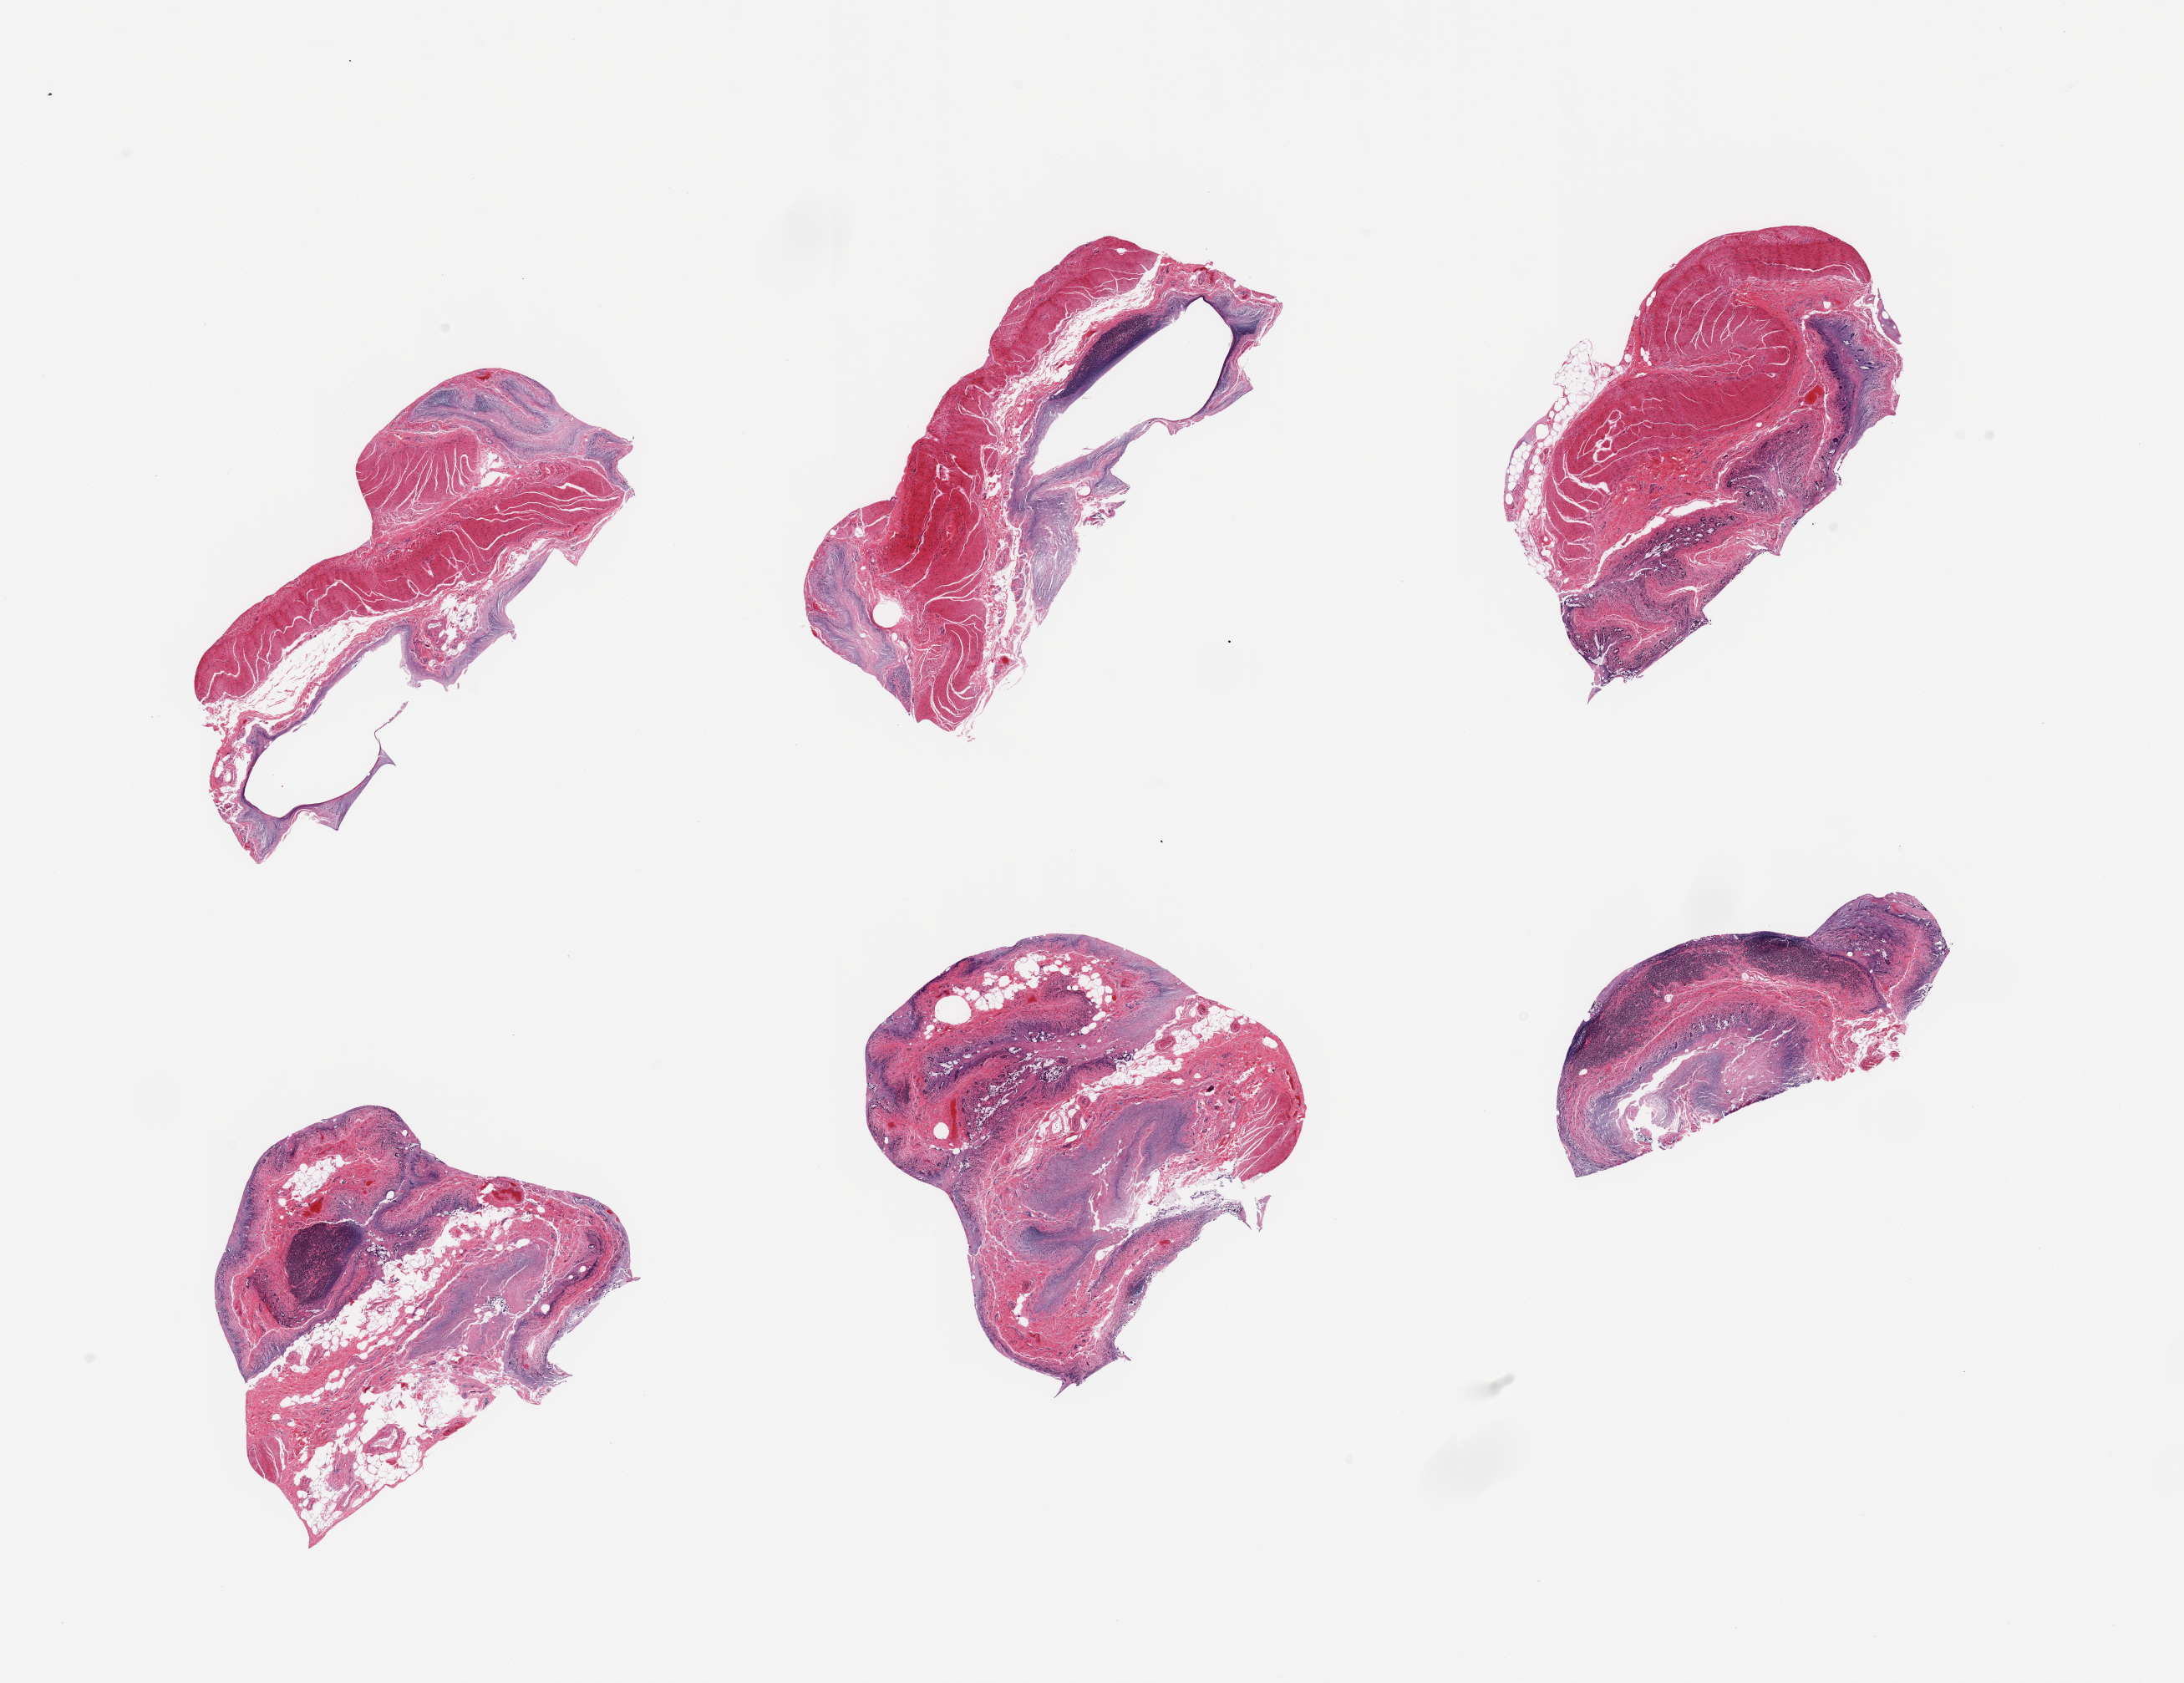
Whole-slide image, haematoxylin and eosin stain, brightfield, low-resolution overview of the scanned area, about 20.7 x 15.9 mm (acquisition: 20x scan). Donor sex: male.
Specimen: PAXgene-fixed paraffin-embedded (PFPE) section; target tissue: ileum; donor tissue sample.